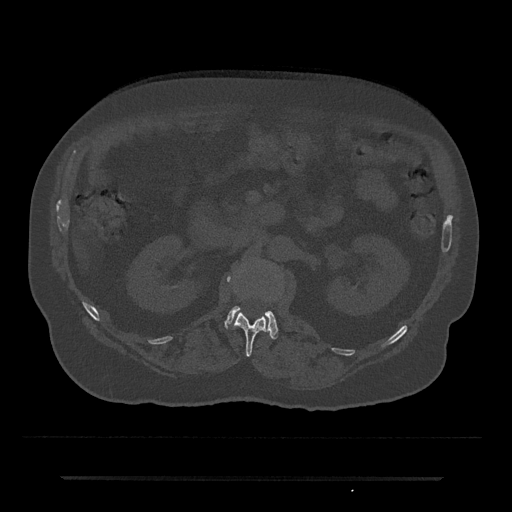
CT including the spine, one axial slice. Slice 44 of 797 in the series (ordered by position). Reconstruction kernel Br40s/3. Bone window (W 1800 / L 400 HU). 512 × 512 image matrix, field of view 437 × 437 mm. Patient: male, 69 years. From the clinical record (not read from this slice): primary cancer: prostate.
Structures marked on this image (semi-automatic segmentation, software-assisted and operator-edited):
- L1 vertebra: bounding box (x1, y1, x2, y2) in pixels: (227, 276, 268, 357)
- L2 vertebra: (225, 306, 278, 339)